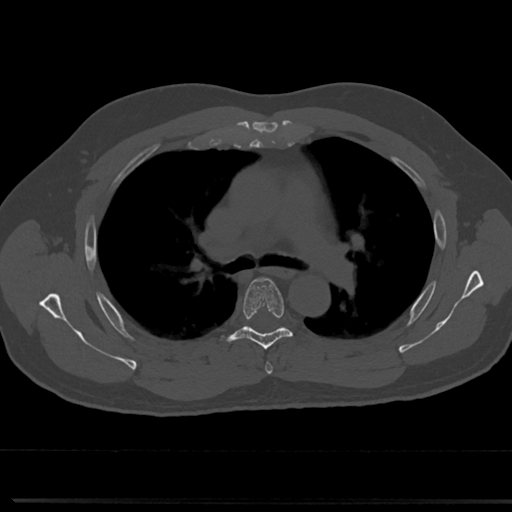
CT including the spine, one axial slice; position 501 of 817 along the scan axis; reconstruction kernel Br40s/3; 120 kVp; bone window (W 1800 / L 400 HU); 0.5 mm slice thickness; 512 × 512 image matrix, field of view 355 × 355 mm. Patient: male, 61 years. From the clinical record (not read from this slice): primary cancer: prostate.
Structures marked on this image (semi-automatically segmented with operator editing):
- T4 vertebra: bounding box (x1, y1, x2, y2) in pixels: (264, 353, 273, 374)
- T5 vertebra: (218, 276, 309, 352)